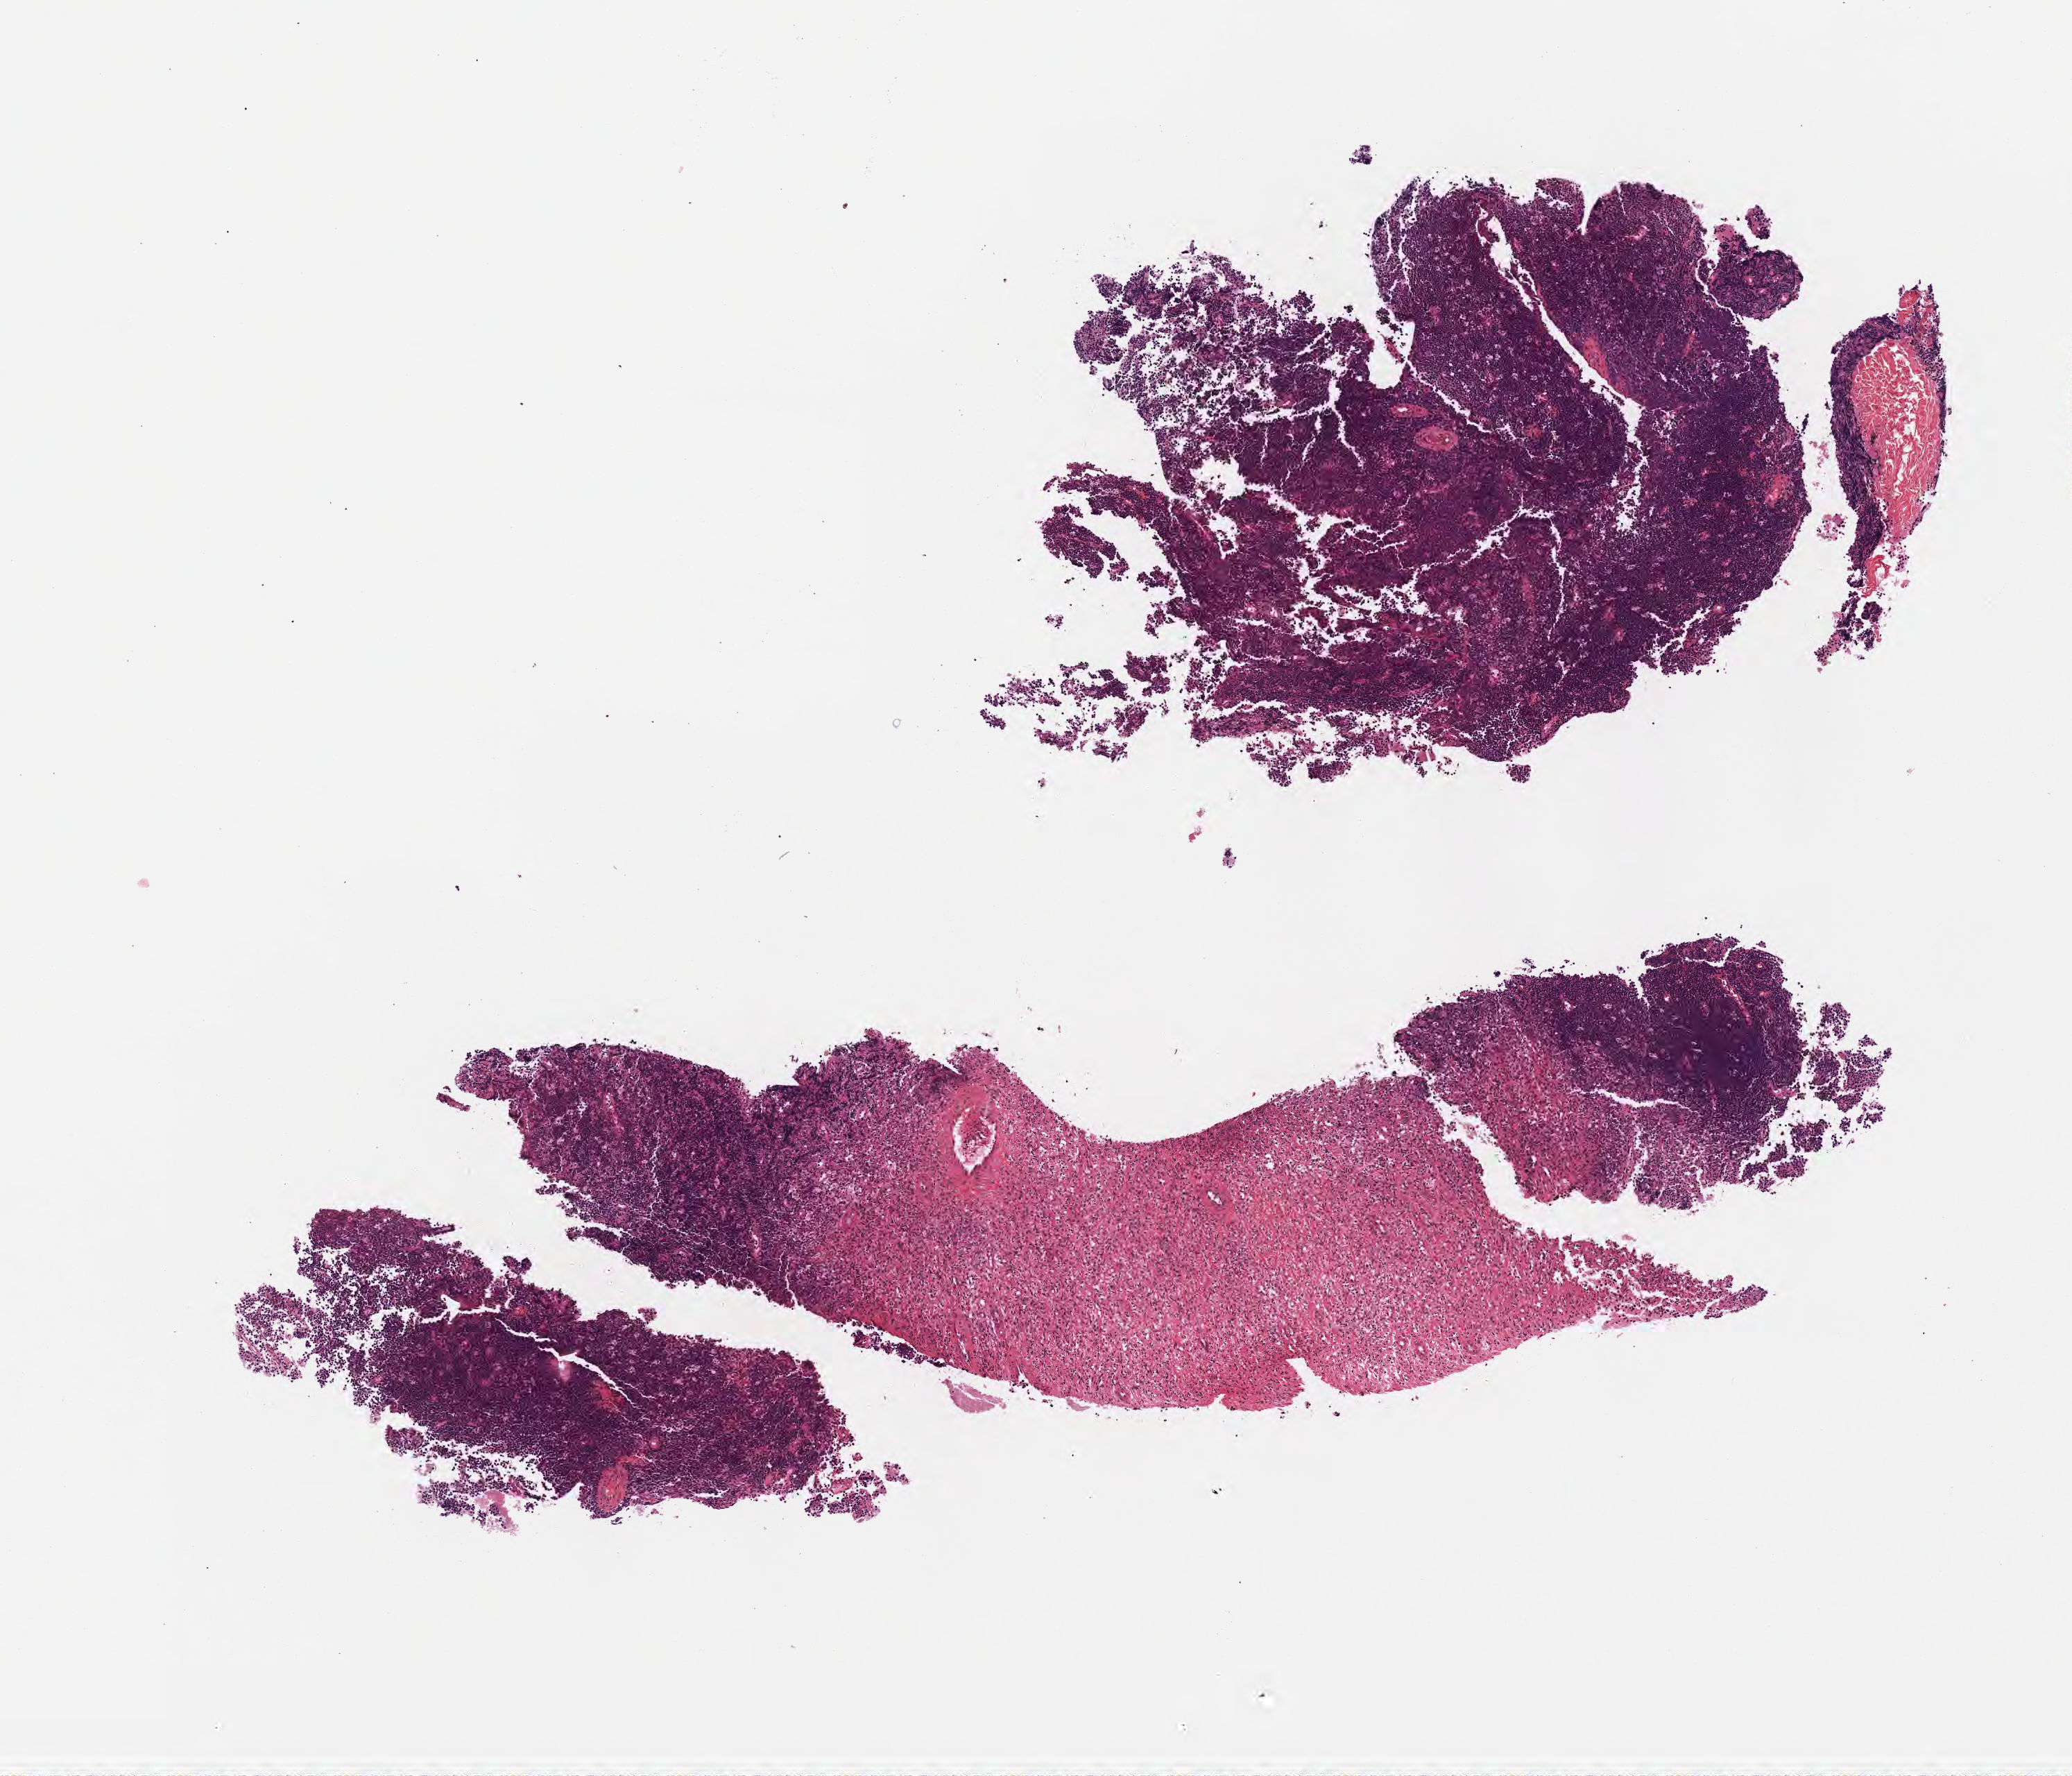
Haematoxylin and eosin whole-slide image — whole scanned area (about 6.0 x 5.2 mm) shown as a low-resolution overview, specimen: tumor tissue, anatomic site: cranium. Male patient; age at initial diagnosis 4 years.
• histologic diagnosis: Burkitt lymphoma, NOS